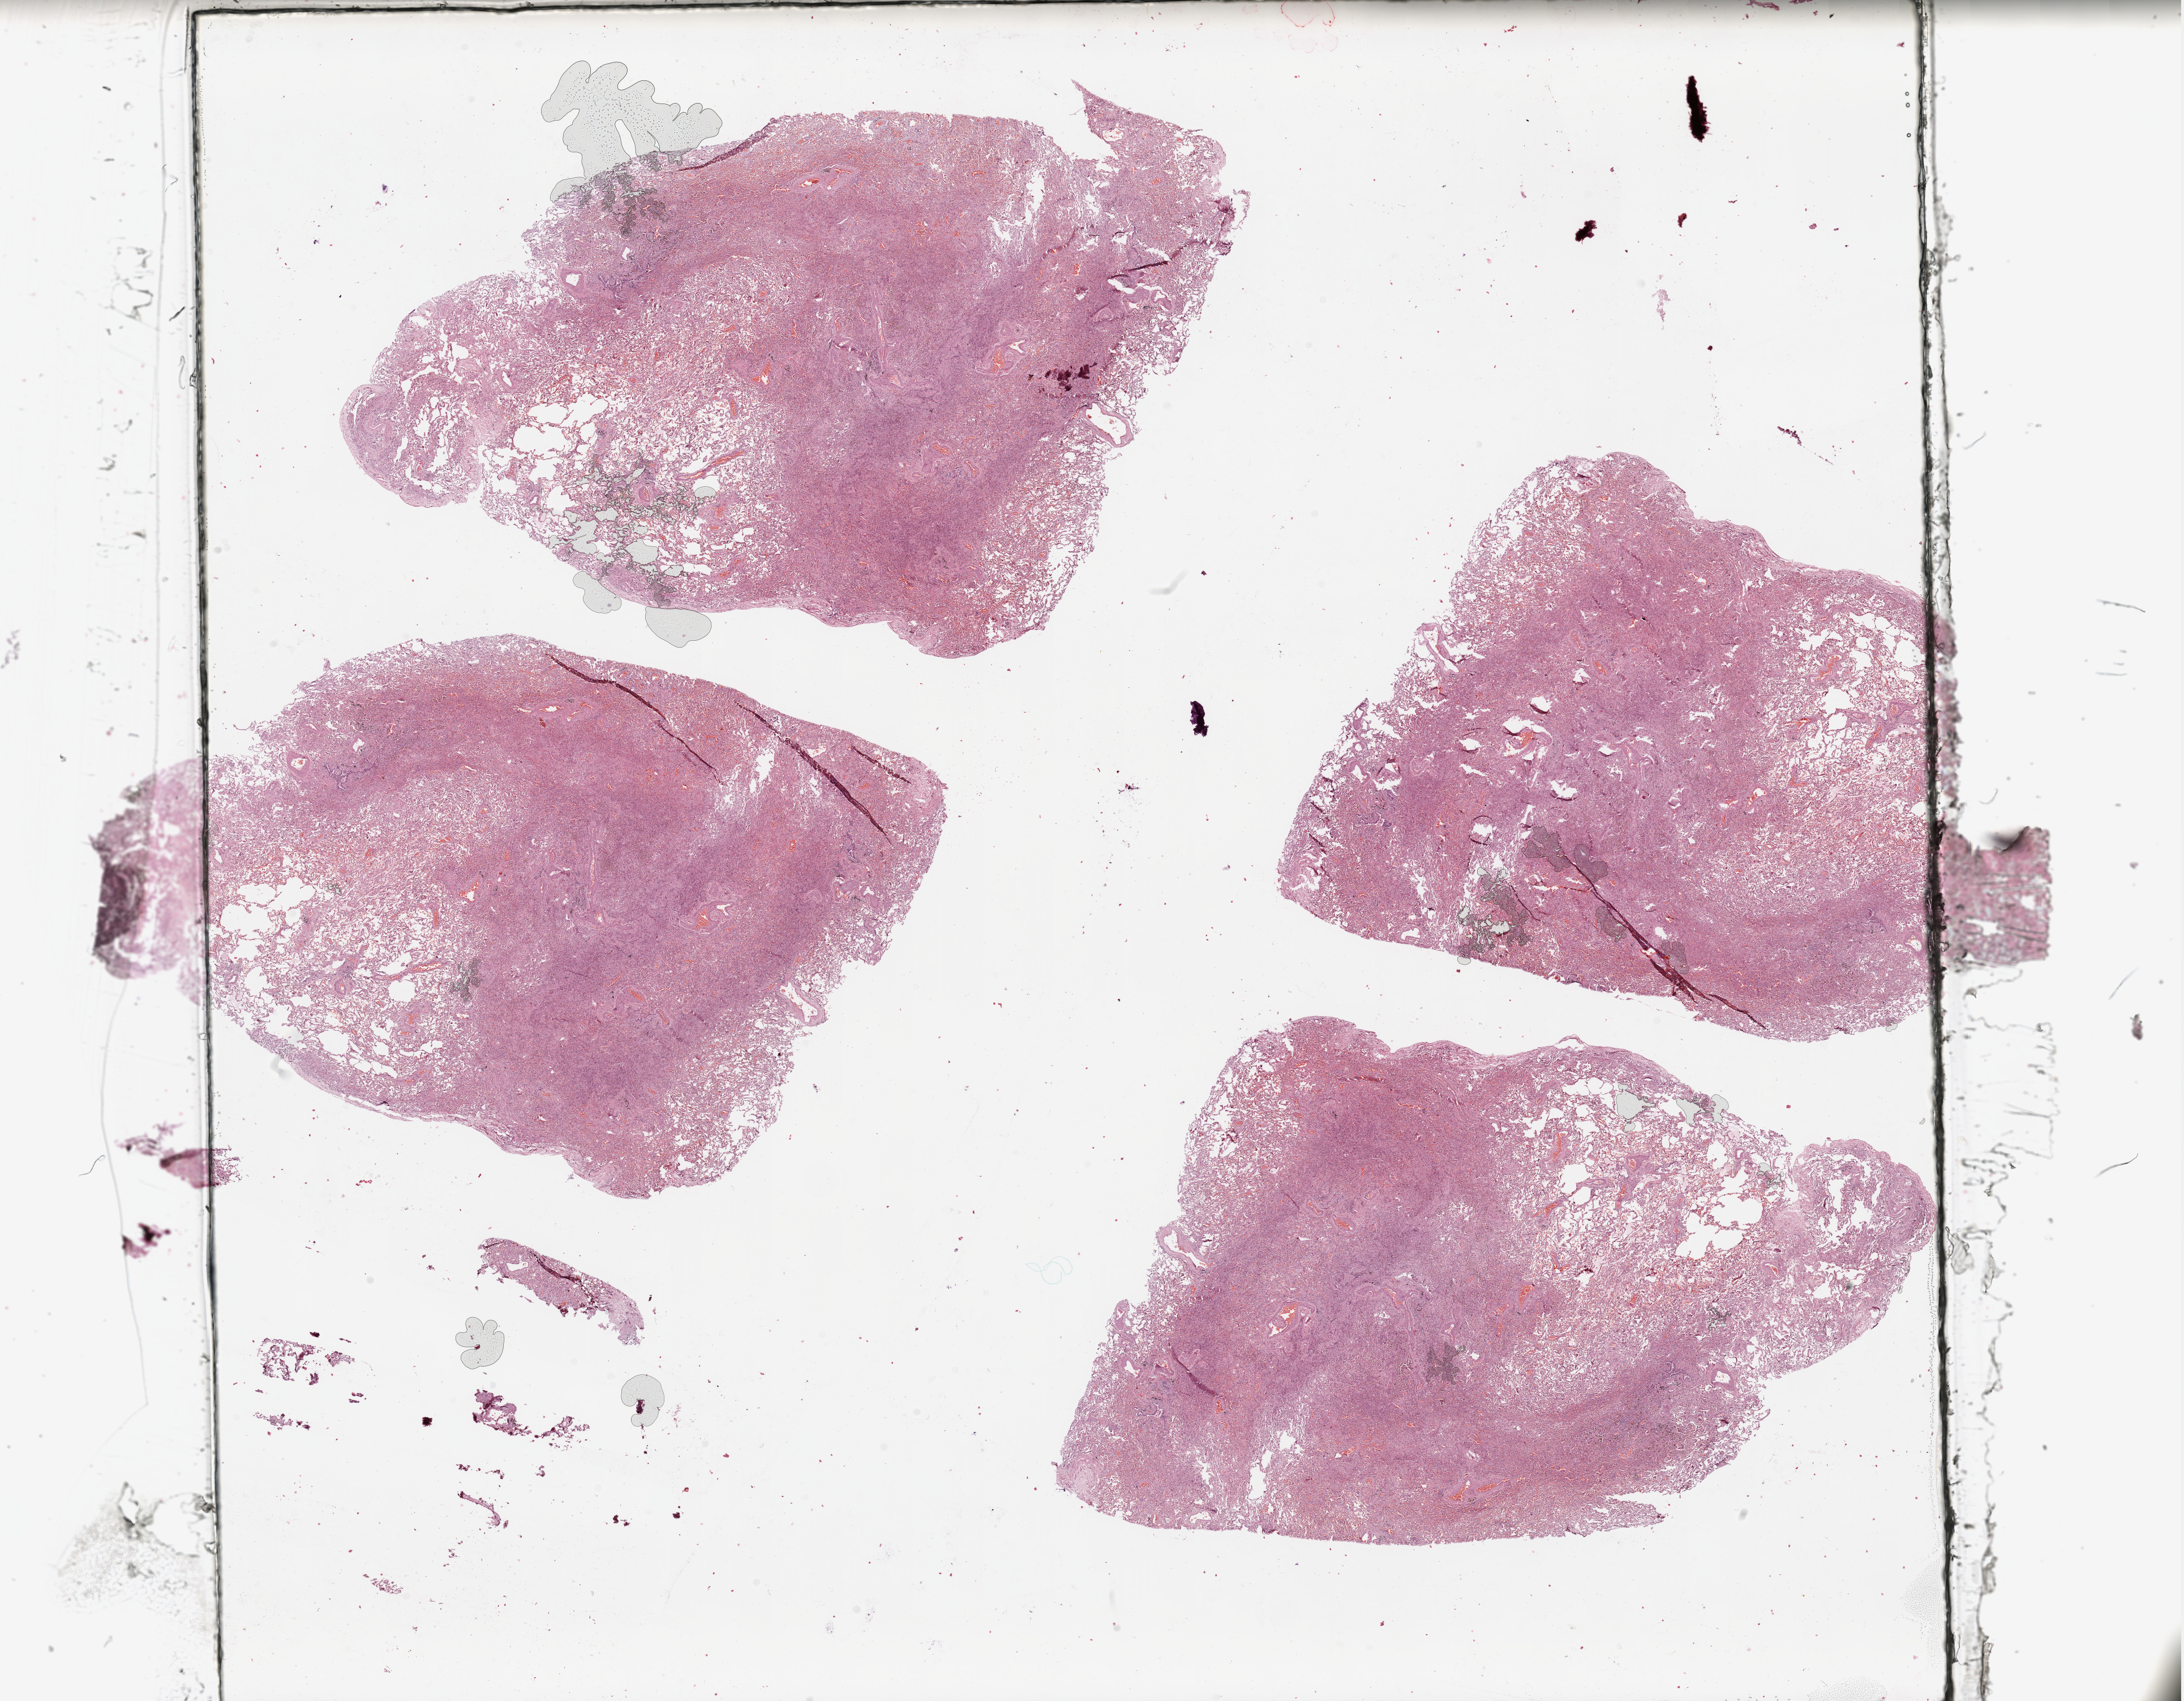
Whole-slide histology image, H&E-stained, whole scanned area (about 30.5 x 23.8 mm, from a 20x scan) shown as a low-resolution overview. Normal (non-tumour) tissue sample, sampled site: lung. 54-year-old male patient.
- this section: normal (non-tumour) tissue from the same patient
- patient diagnosis: Adenocarcinoma, NOS